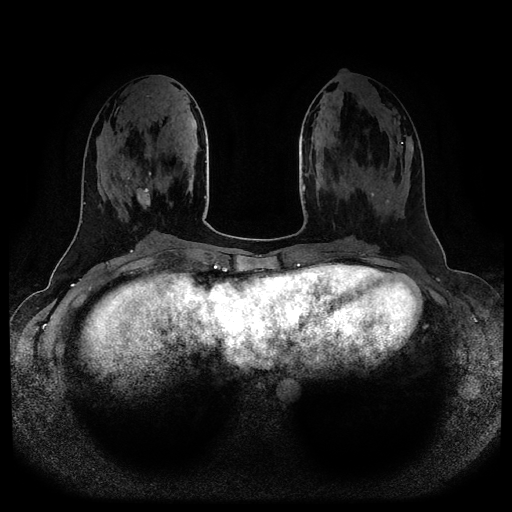
Breast MRI (dynamic contrast-enhanced, multi-phase), one axial slice. Position 39 of 116 along the scan axis. Dynamic contrast-enhanced series, time point 2 of 5 at this slice position (early post-contrast). 1.5 T. TE 2.6 ms, TR 5.2 ms. 2 mm slice thickness. 512 × 512 image matrix, field of view 380 × 380 mm. Female patient, age 25 years.
Annotated regions visible in this slice (semi-automatically segmented with operator editing):
- breast lesion (labelled benign in the annotation): box from (x=133, y=188) to (x=151, y=210) px